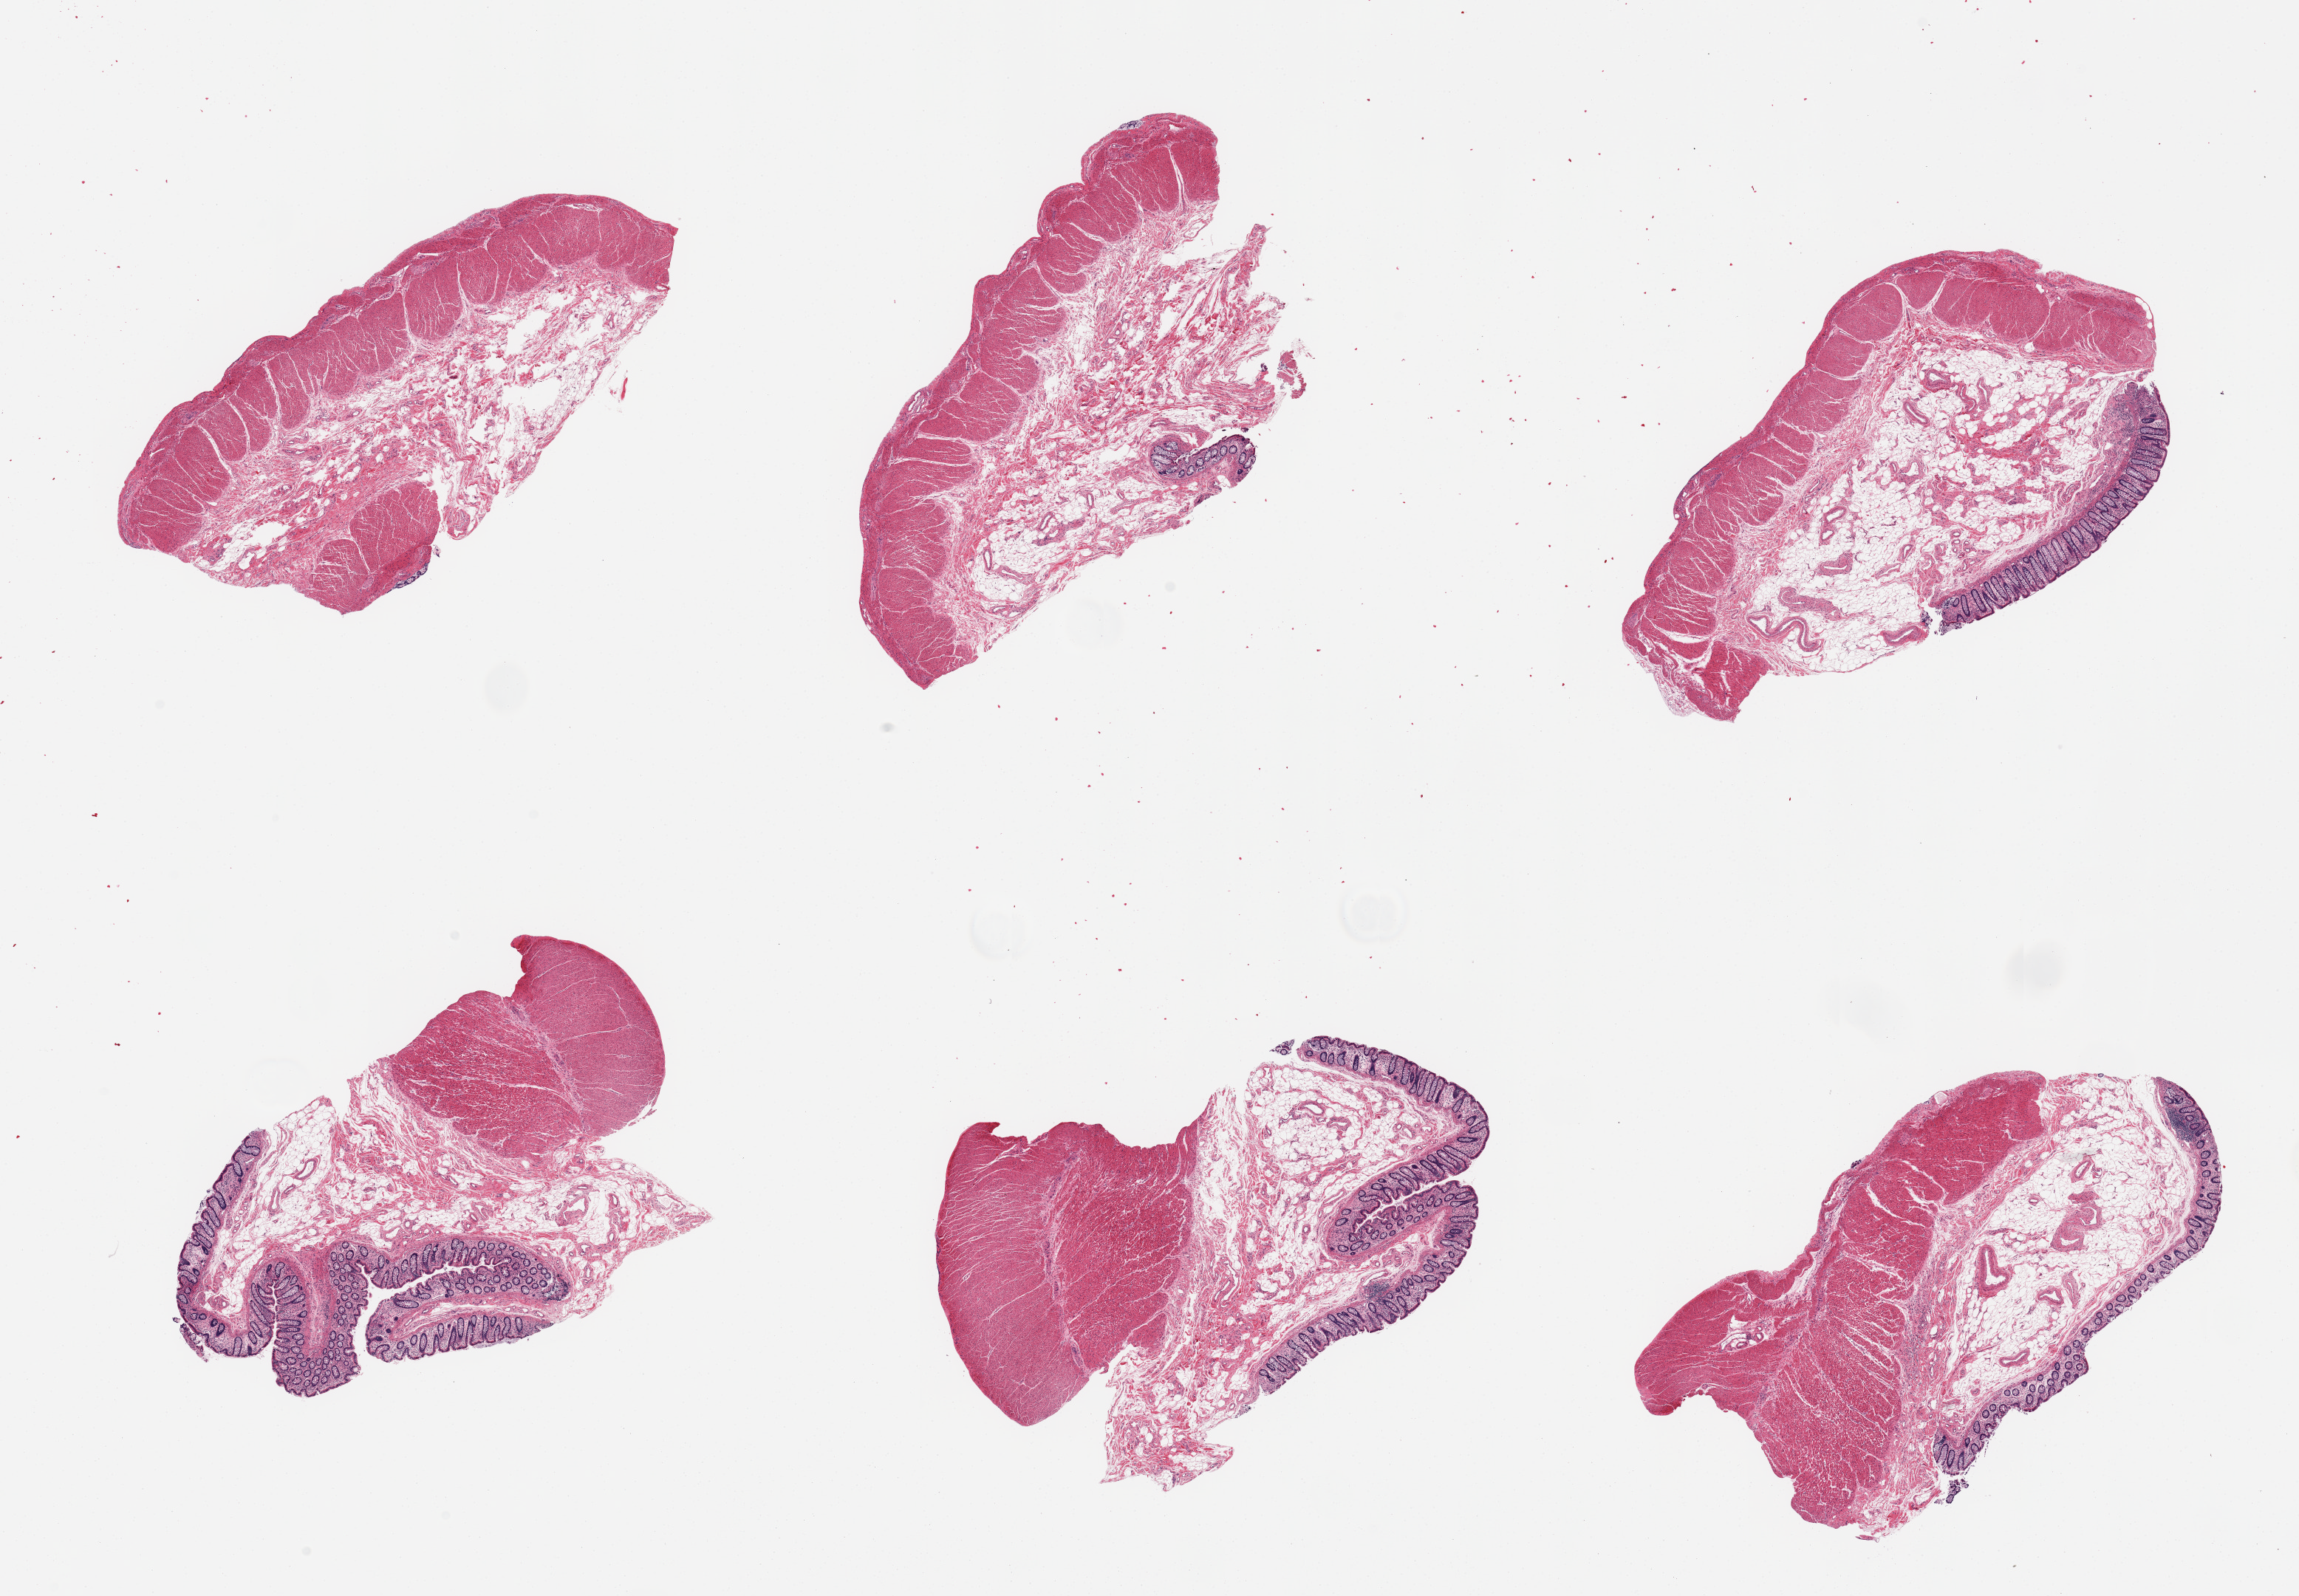
Whole-slide image, H&E stain, brightfield — a low-resolution overview of the entire scanned area, about 24.6 x 17.1 mm (slide scanned at 20x); PAXgene-fixed paraffin-embedded (PFPE) section; target tissue: transverse colon; donor tissue sample. Male donor.
* pathologist's review note for this sample: 6 pieces; 5 full thickness, 1 without mucosa